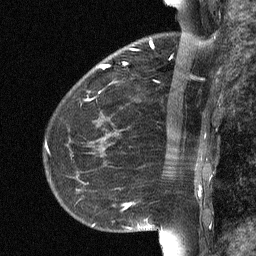
Breast MRI (dynamic contrast-enhanced), one sagittal slice; slice 21 of 64 in the series (ordered by position); dynamic contrast-enhanced study with each time point stored as its own series, time point 2 of 3 at this slice position (early post-contrast, ordered by acquisition time); 1.5 T; TE 4.8 ms, TR 27 ms; 2 mm slice thickness; 256 × 256 image matrix. Patient: female, 51 years. From the clinical record (not read from this slice): setting: breast cancer imaged before/during neoadjuvant chemotherapy; receptor status: HR-positive, HER2-negative.
Structures marked on this image (semi-automatically segmented with operator editing):
- analysis volume of interest (the breast-tissue region the enhancement analysis was run in; not a lesion): bounding box <72,34,182,118> (left, top, right, bottom; pixels)
- tumour enhancement mask (voxels above the 90 % enhancement threshold inside the analysis volume of interest): <100,42,153,69>